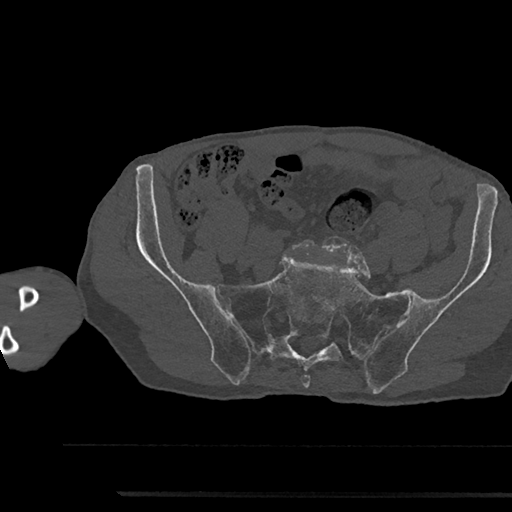
CT including the spine, one axial slice; reconstruction kernel Br40s/3; 120 kVp; bone window (W 1800 / L 400 HU); 0.5 mm slice thickness; 512 × 512 image matrix. Patient: male, 79 years. Case-level facts recorded for this patient, not image findings: primary cancer: prostate.
Outlined on this slice (semi-automatically segmented with operator editing):
- L5 vertebra: bounding box (x1, y1, x2, y2) in pixels: (291, 239, 315, 249)